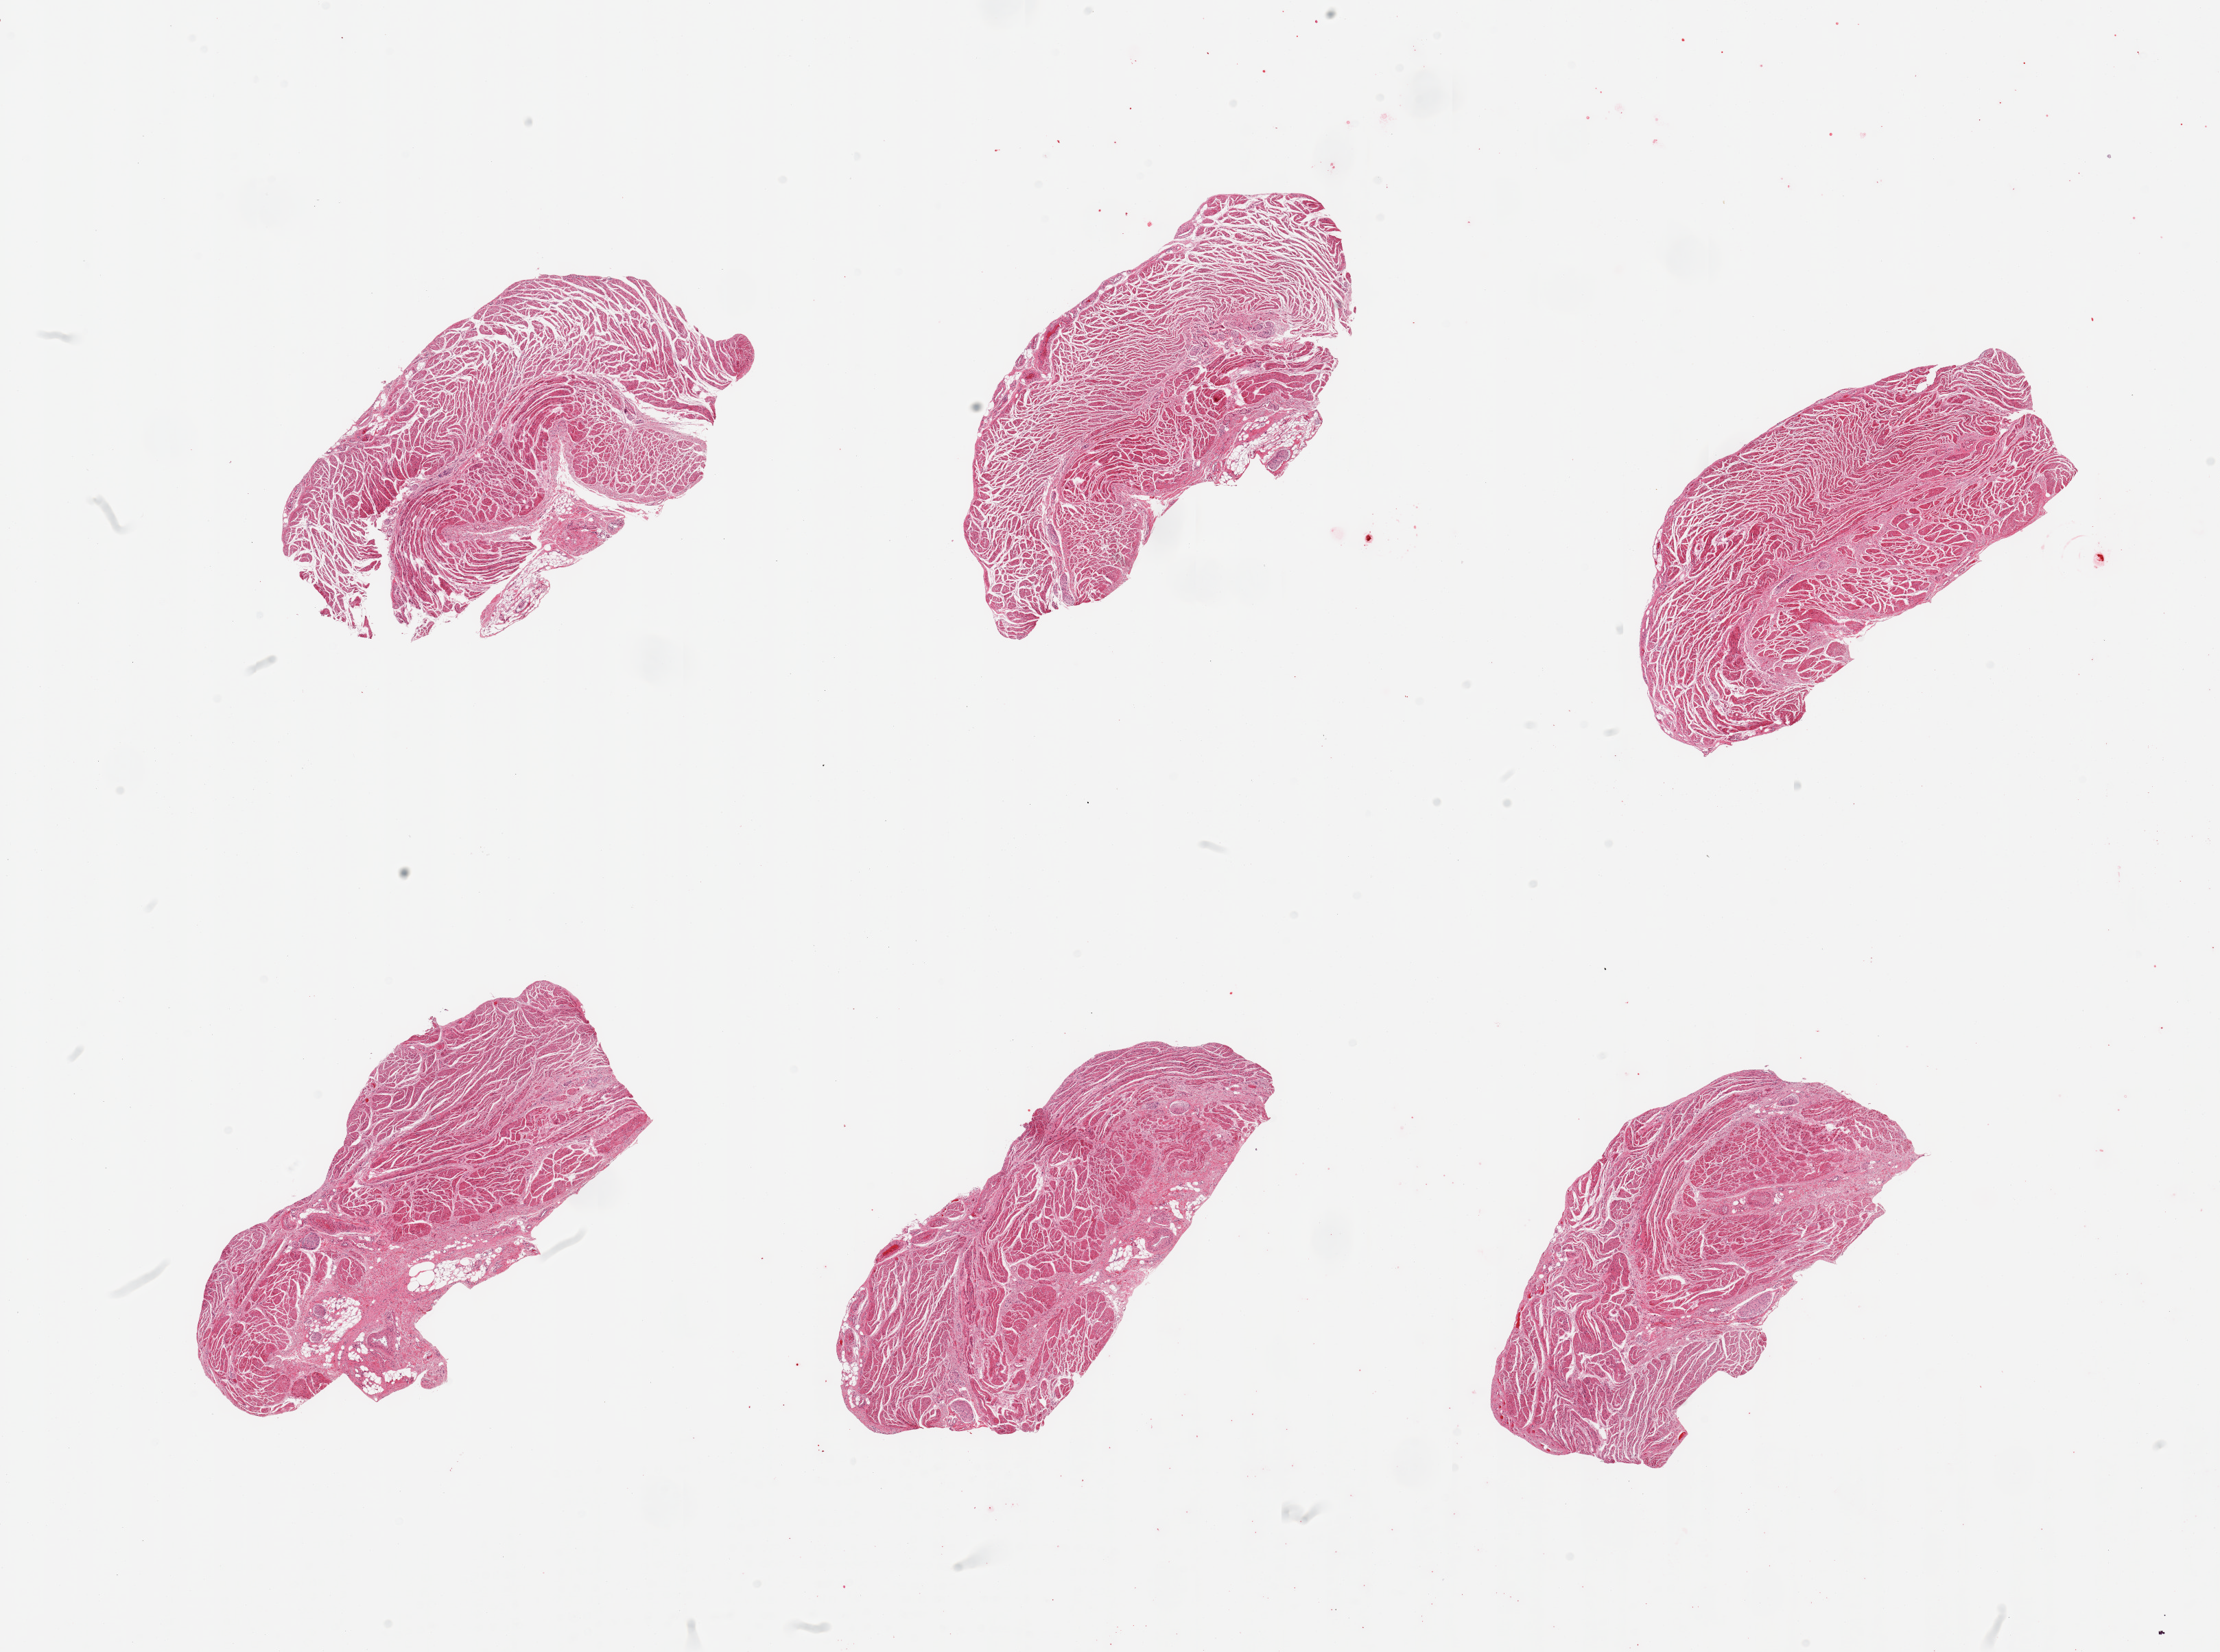
Whole-slide image, hematoxylin and eosin (H&E) stain, brightfield — shown as a low-resolution overview of the whole scanned area (about 25.6 x 19.0 mm, slide scanned at 20x); PAXgene-fixed, paraffin-embedded tissue; section of gastroesophageal junction (target tissue); tissue donor sample. Donor sex: male.
Reviewer comment on this tissue sample: 6 pieces; well dissected muscle.